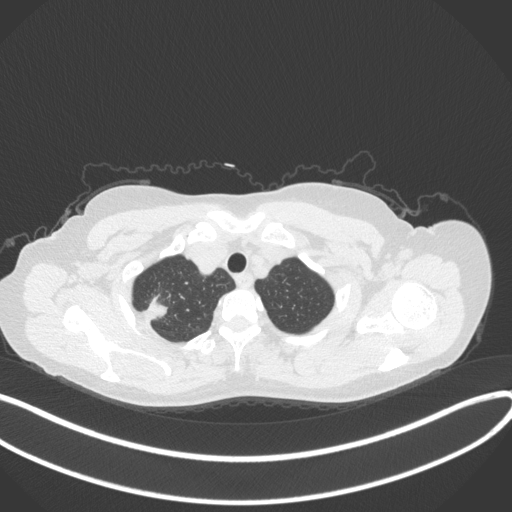
Chest CT, one axial slice. Position 323 of 342 along the scan axis. Reconstruction kernel B31f. Lung window (W 1500 / L -600 HU). 1 mm slice thickness. 512 × 512 image matrix, field of view 400 × 400 mm. Female patient, age 50 years. From the clinical record (not read from this slice): clinical TNM (as recorded): T1c N0 M0; histopathological grade: G2-3.
Structures marked on this image (bounding box drawn by a radiologist):
- lung tumour (recorded histology: adenocarcinoma): box from (x=141, y=296) to (x=168, y=323) px